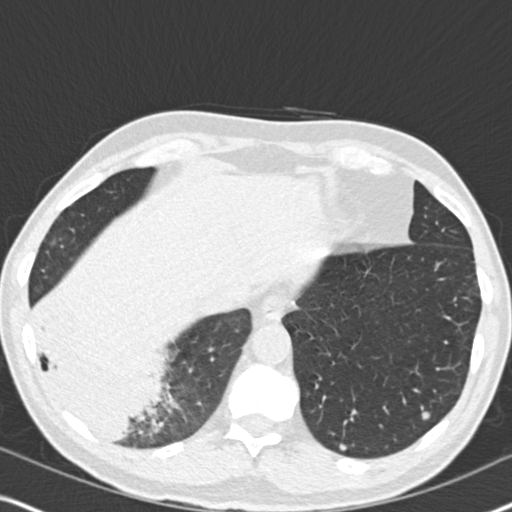
Low-dose screening chest CT, one axial slice. Position 53 of 182 along the scan axis. Reconstruction kernel B30f. Lung window (W 1500 / L -600 HU). 2 mm slice thickness. 512 × 512 image matrix.
Outlined on this slice (manually delineated by an expert):
- lesion 1 (tumor, lower lobe of right lung): bounding box <43,346,162,436> (left, top, right, bottom; pixels)